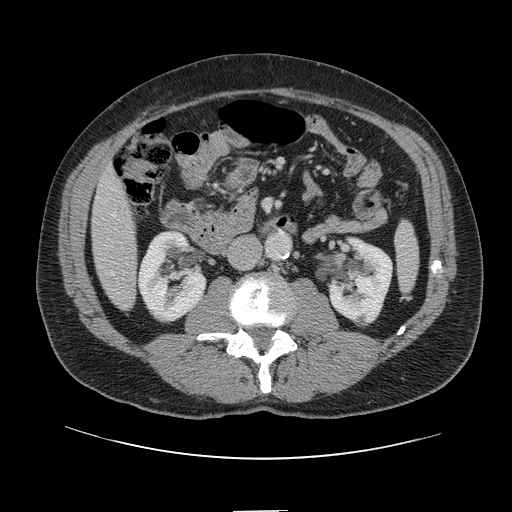
Contrast-enhanced abdominal CT, one axial slice. Slice 25 of 161 in the series (ordered by position). 120 kVp. Soft-tissue window (W 400 / L 40 HU). 2.5 mm slice thickness. 512 × 512 image matrix, field of view 412 × 412 mm. Male patient, age 66 years. From the clinical record (not read from this slice): diagnosis: colorectal cancer liver metastases, imaged before liver resection; multiple liver metastases: no; largest metastasis: 3.5 cm; chemotherapy before resection: yes.
Outlined on this slice (manually delineated by an expert):
- hepatic veins: bounding box (x1, y1, x2, y2) in pixels: (112, 214, 115, 275)
- liver: (93, 169, 137, 309)
- planned liver remnant (the part of the liver to remain after resection): (93, 169, 134, 256)